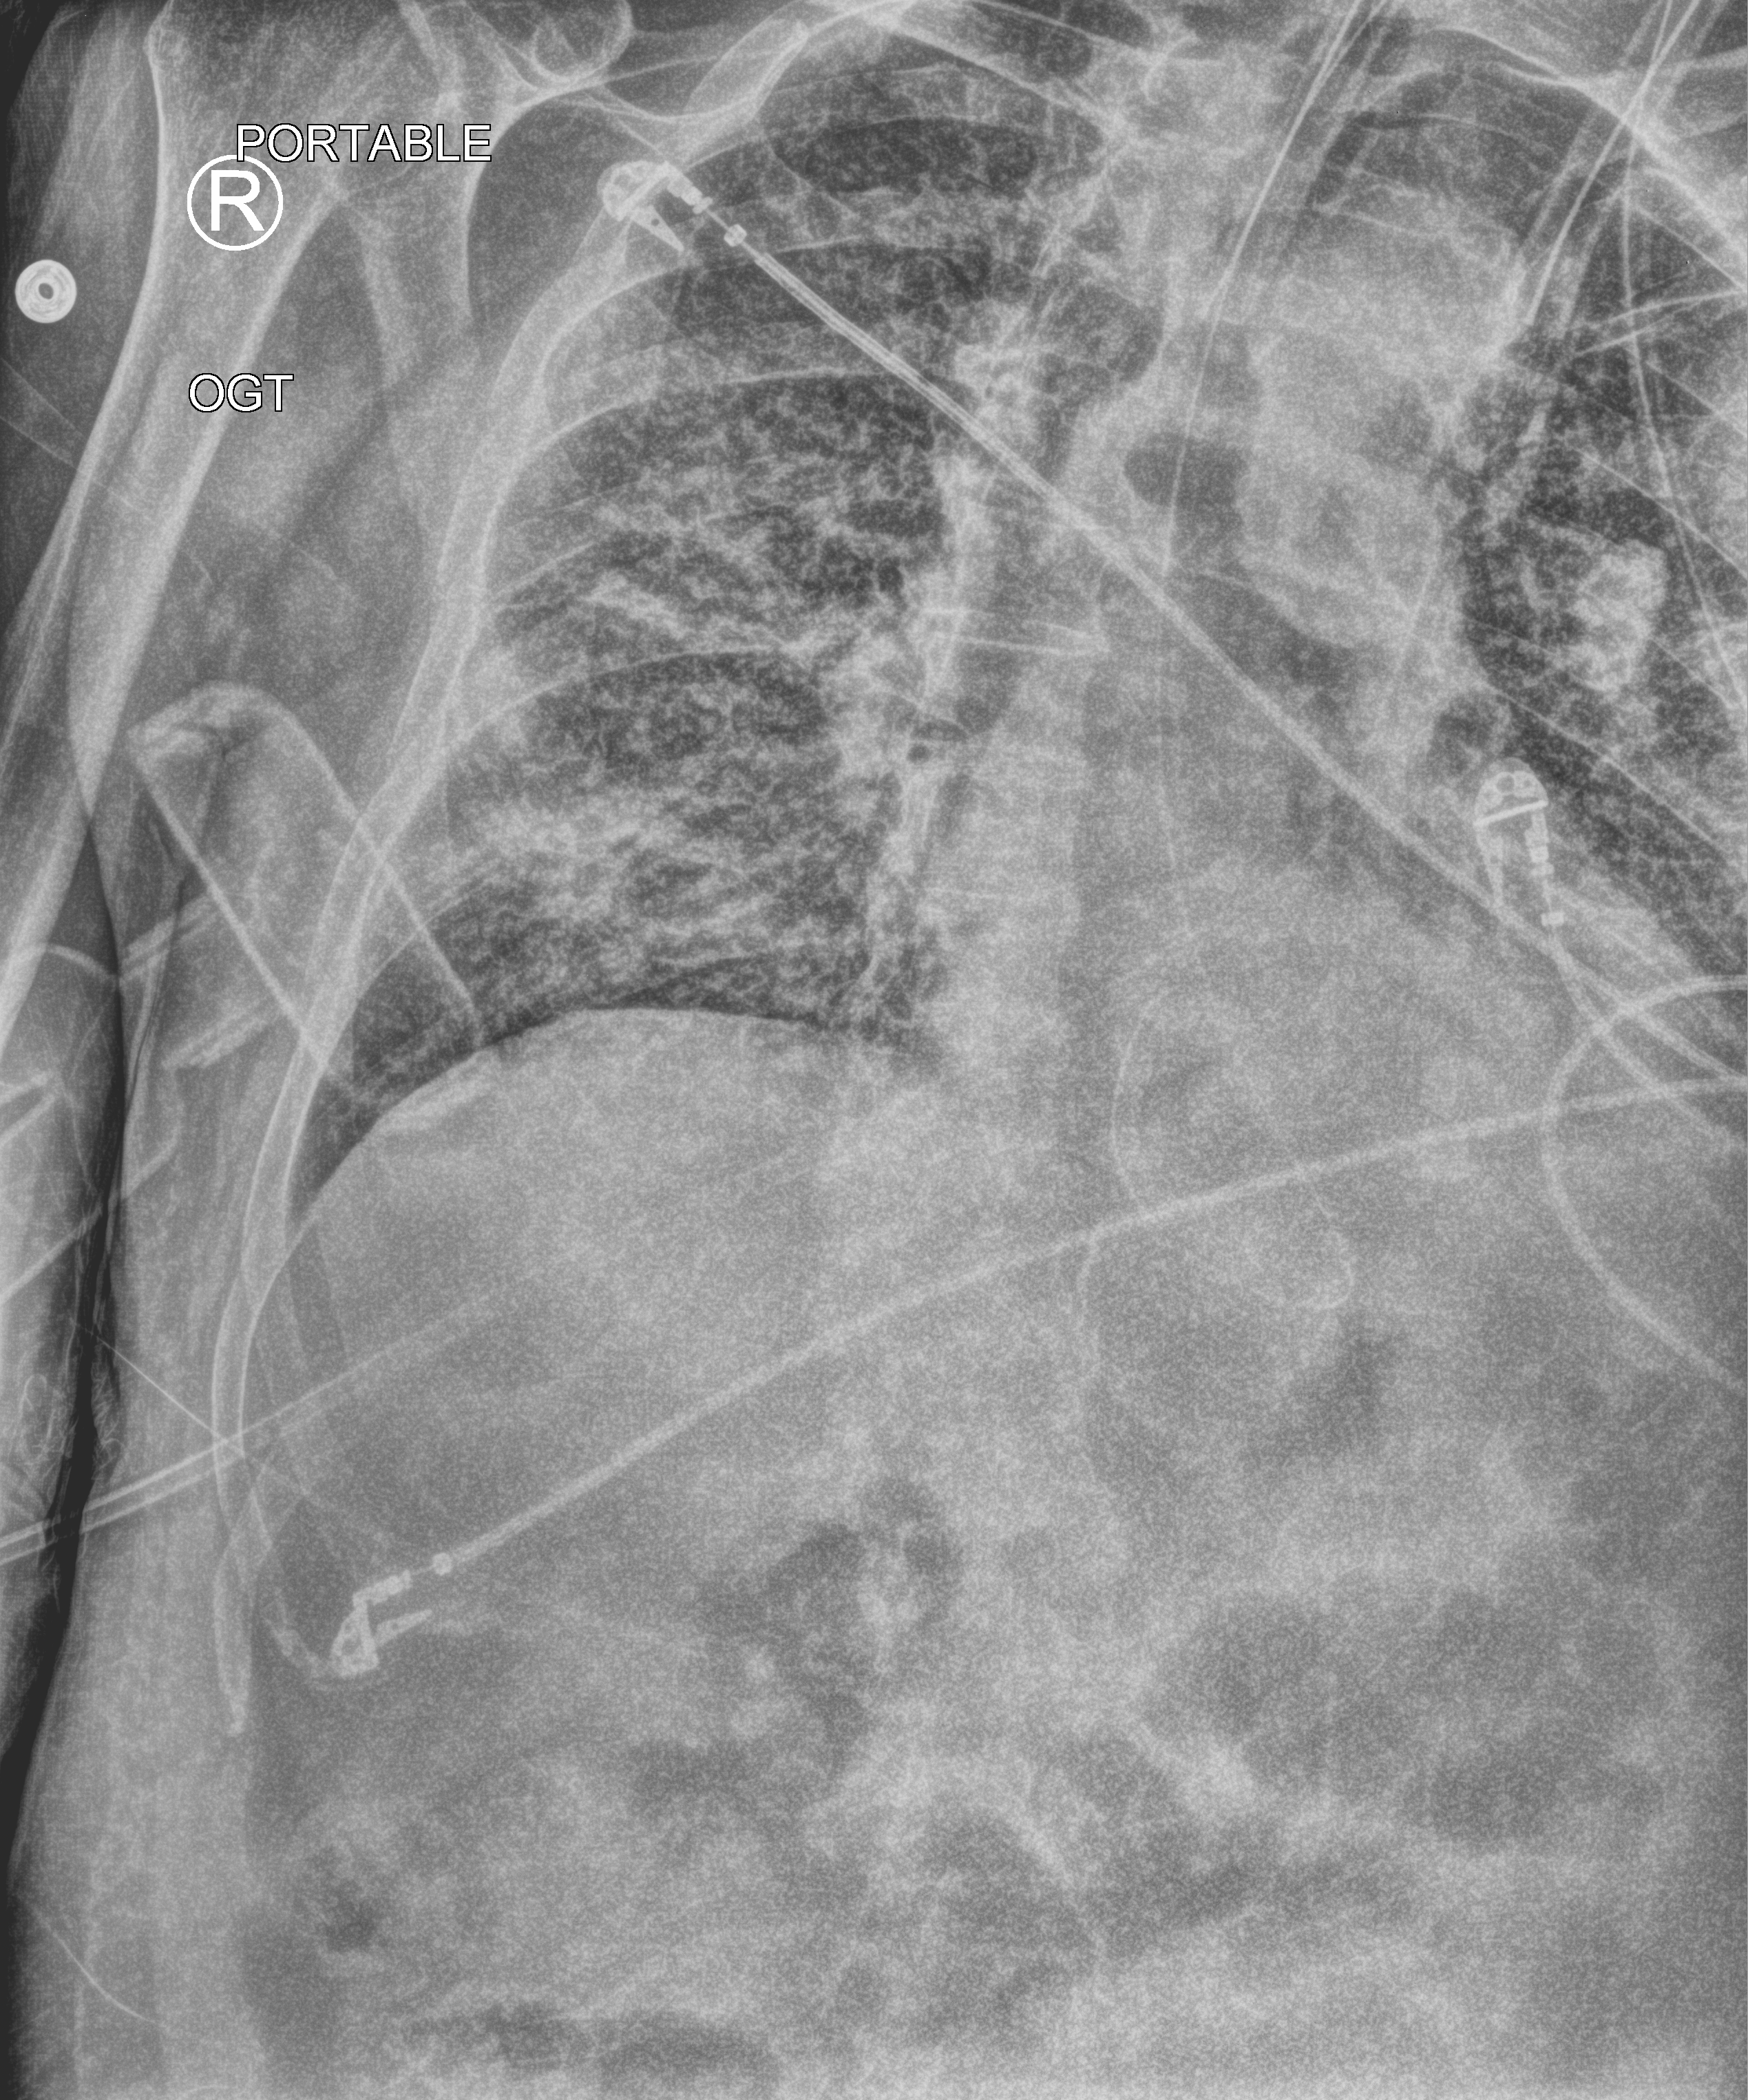
Bedside chest radiograph (computed radiography), anteroposterior (AP) projection. Patient hospitalised with COVID-19; male, aged 75–90 years.
From the hospital-stay record, not from the radiograph (when in the stay this image was taken is not recorded):
- chronic kidney disease (admission record): no